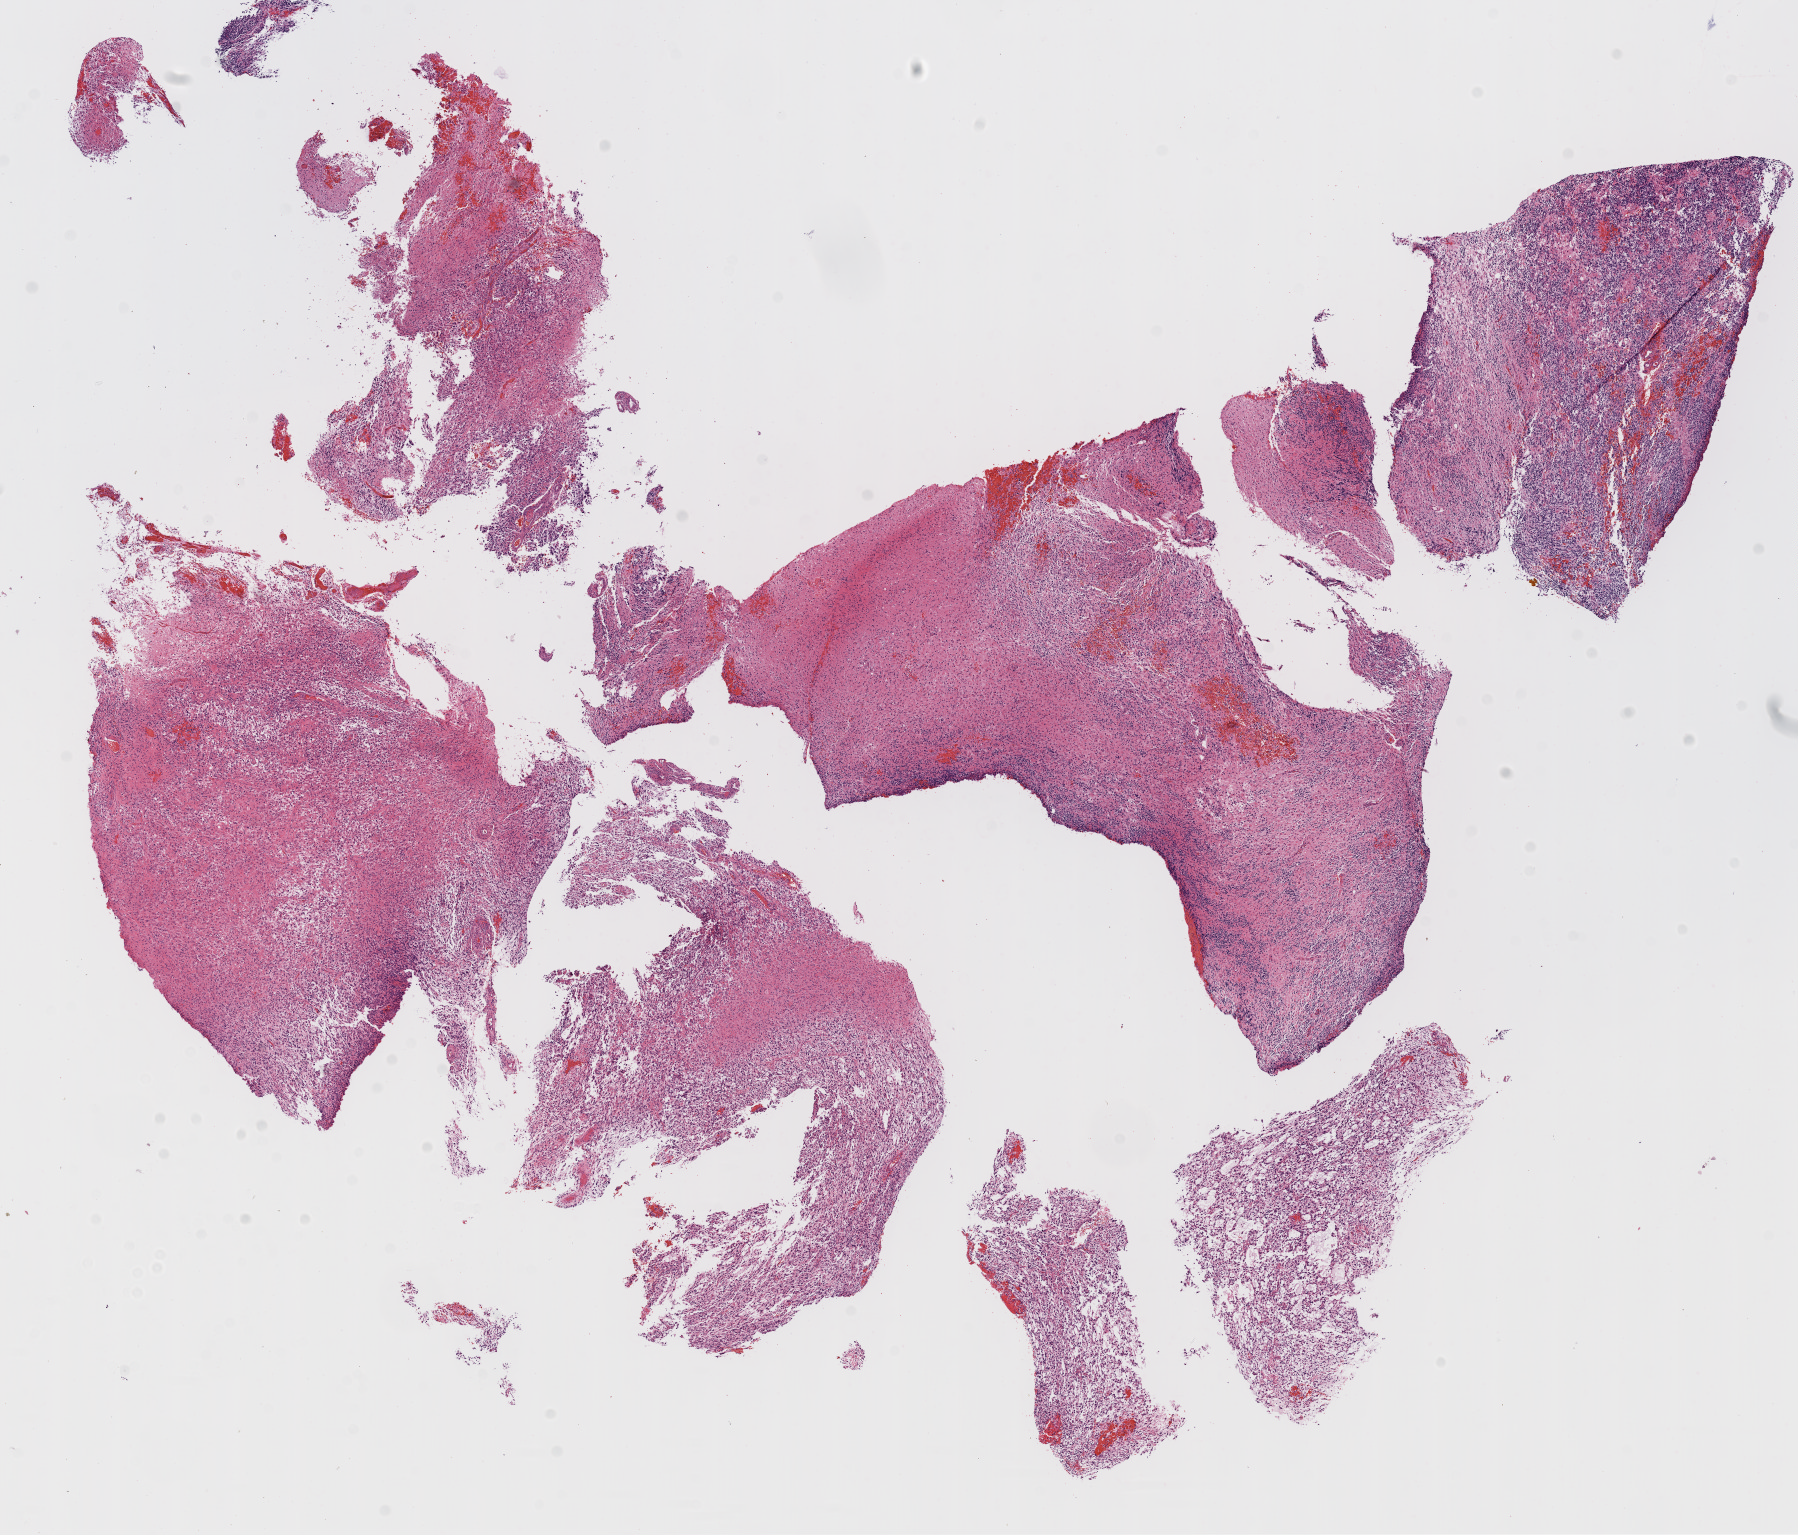
Whole-slide histology image, H&E-stained — a low-resolution overview of the entire scanned area, about 14.5 x 12.4 mm (acquisition: 20x scan), formalin-fixed paraffin-embedded (FFPE) diagnostic section, brain, primary tumour sample. Male, age 31 years at initial diagnosis.
Histologic diagnosis: Glioblastoma.